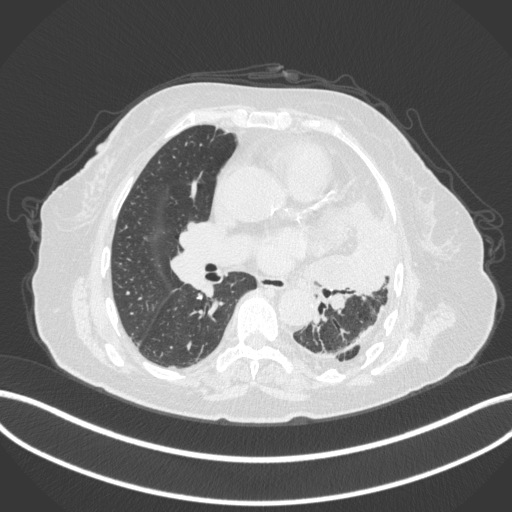
Chest CT, one axial slice; position 191 of 399 along the scan axis; reconstruction kernel B31f; lung window (W 1500 / L -600 HU); 1 mm slice thickness; 512 × 512 image matrix. Female patient, age 75 years. Case-level facts recorded for this patient, not image findings: clinical TNM (as recorded): T3 N3 M1.
Structures marked on this image (rectangle marked by the reading radiologist):
- lung tumour (recorded histology: adenocarcinoma): bounding box [x1, y1, x2, y2] px = [298, 192, 402, 297]